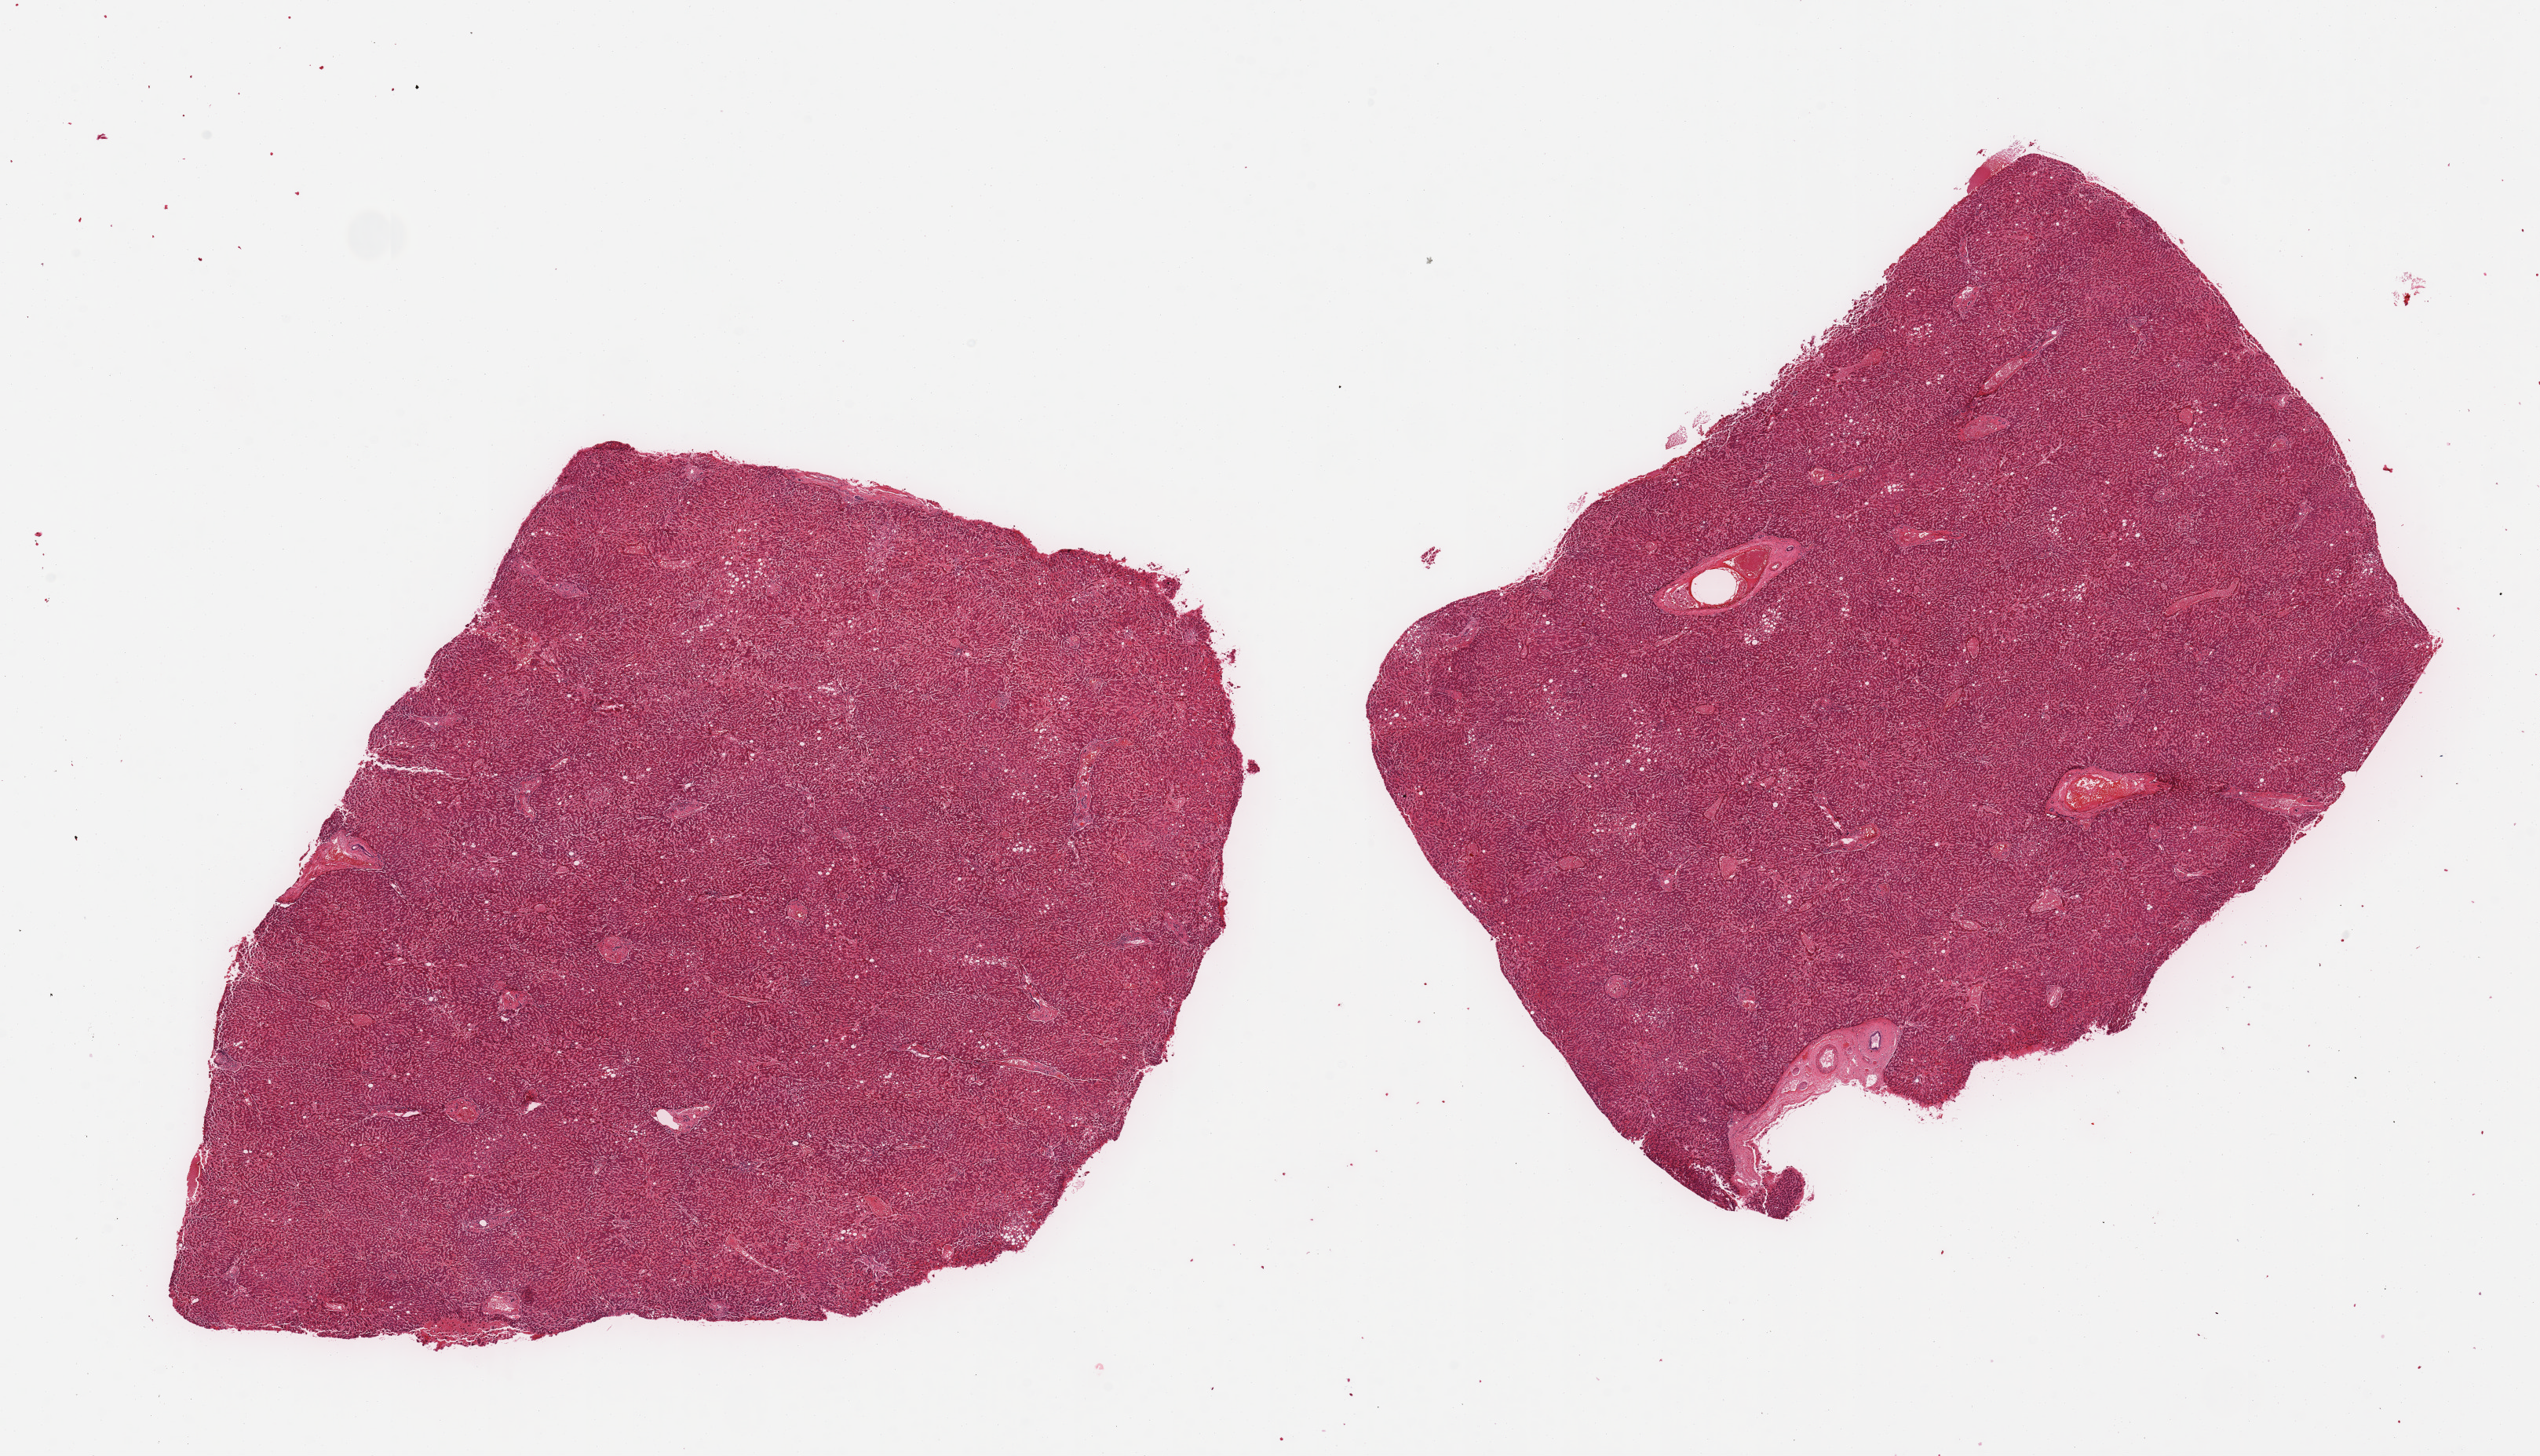
H&E whole-slide image, shown as a low-resolution overview of the whole scanned area (about 25.6 x 14.7 mm); PAXgene-fixed paraffin-embedded (PFPE) section; target tissue: liver; donor tissue sample.
Review note (as recorded): 2 pieces; congestion, mild steatosis.